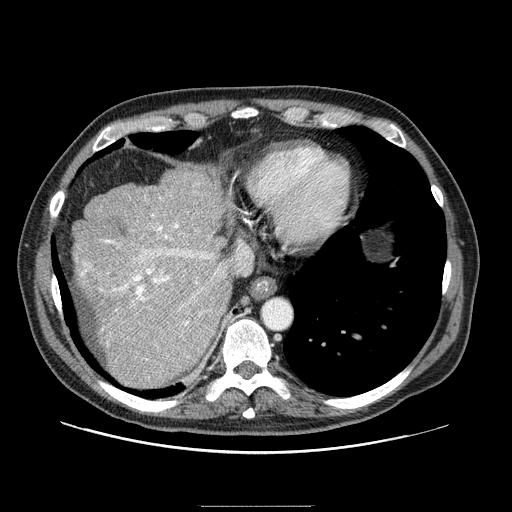
Contrast-enhanced abdominal CT (liver protocol), one axial slice. Reconstruction kernel STANDARD. One of 2 acquisitions stored at this slice position. Soft-tissue window (W 400 / L 40 HU). 512 × 512 image matrix, field of view 400 × 400 mm. Case-level facts recorded for this patient, not image findings: diagnosis: hepatocellular carcinoma (patient treated with transarterial chemoembolisation; whether this scan precedes or follows treatment is not stated here); TNM stage (as recorded): Stage-II; Child-Pugh class: A; tumour size: 3.2 cm.
Structures marked on this image (semi-automatically segmented with operator editing):
- abdominal aorta: box from (x=261, y=298) to (x=291, y=328) px
- liver parenchyma outside the tumour (the mass and vessels are separate outlines, so this box may not span the whole liver): (x=72, y=168)–(x=230, y=388)
- liver vessels: (x=81, y=198)–(x=222, y=360)